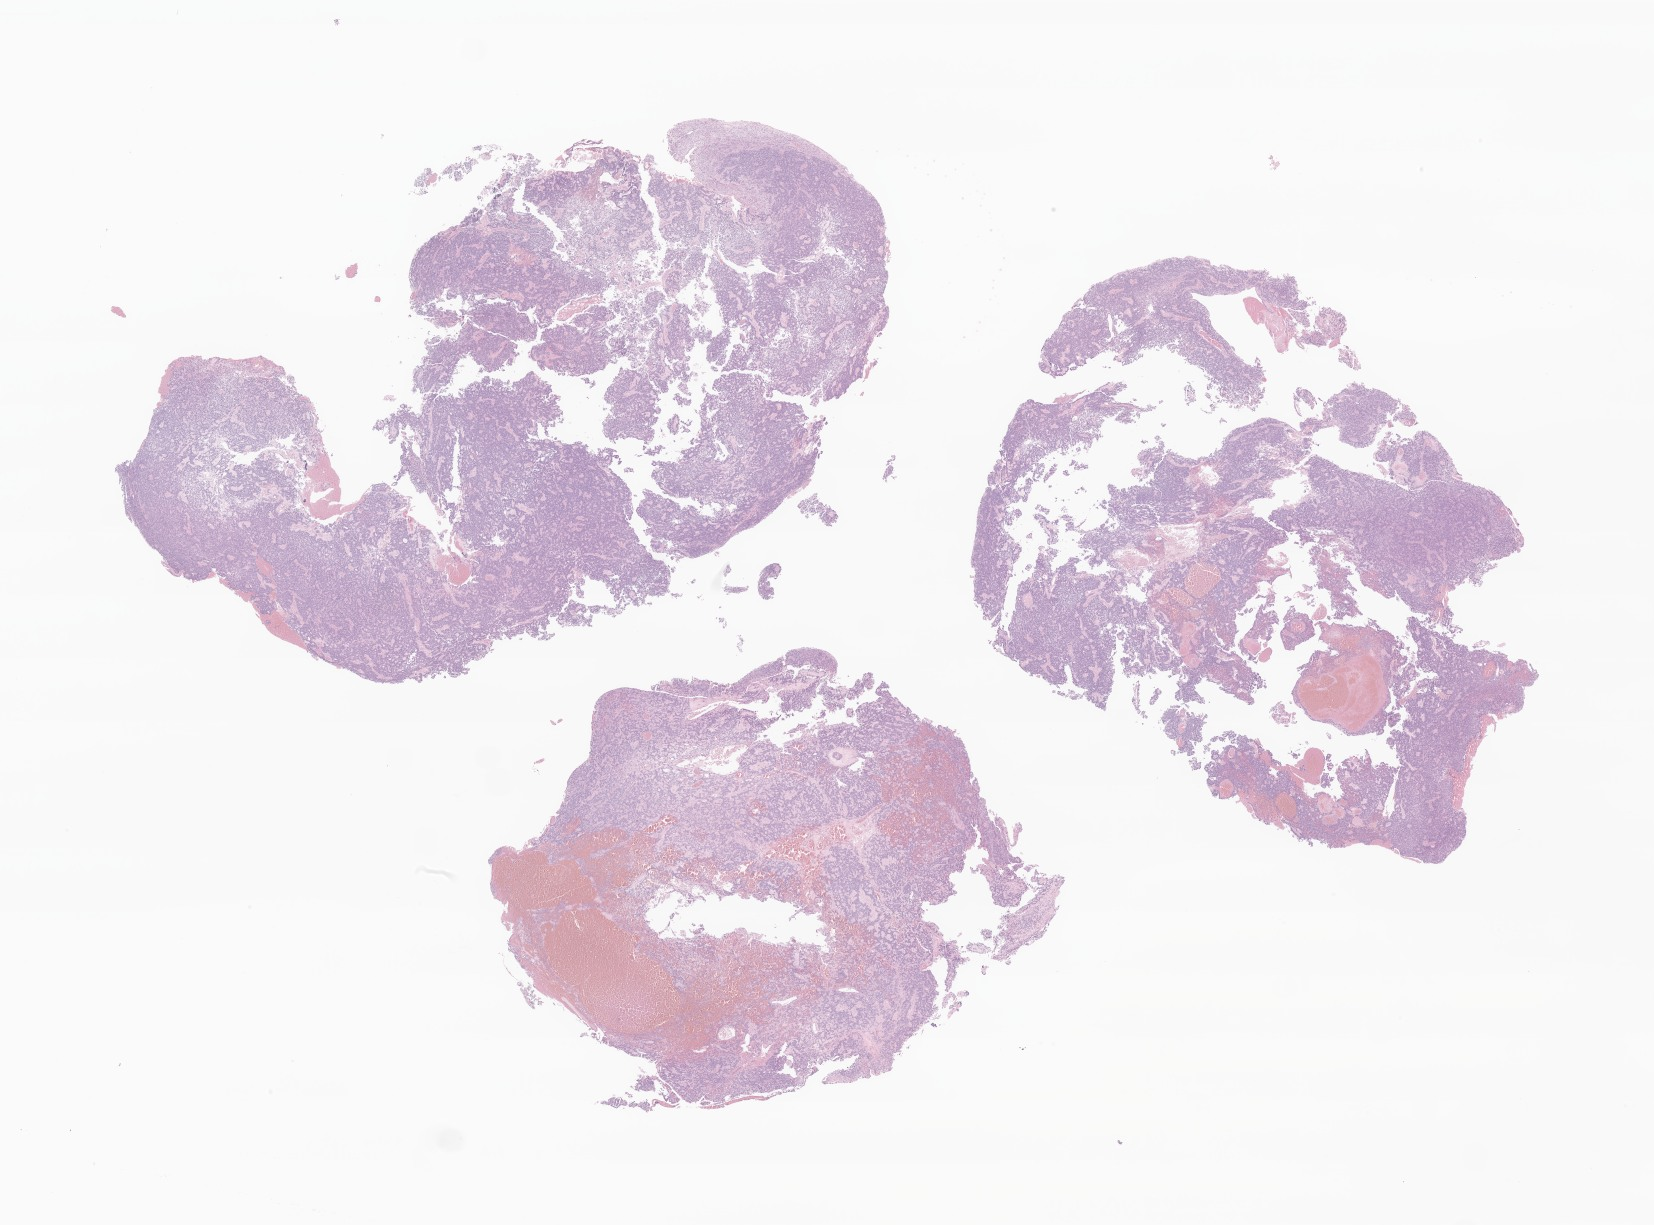
Digitized hematoxylin and eosin (H&E)-stained section of tumor tissue from the brain — whole scanned area (about 27.9 x 20.7 mm) shown as a low-resolution overview. FFPE section. Female patient, age 204 months (17 years).
• recorded diagnosis: Ependymoma, anaplastic